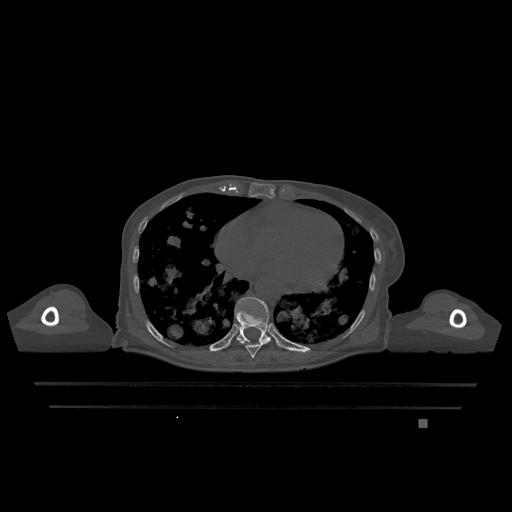
CT including the spine, one axial slice; slice 668 of 1317 in the series (ordered by position); bone window (W 1800 / L 400 HU); 0.5 mm slice thickness; 512 × 512 image matrix, field of view 500 × 500 mm. Patient: female, 74 years. Case-level facts recorded for this patient, not image findings: primary cancer: lung; vertebrae with lytic lesions (as recorded): T1, T4, T5, T6, L4, L5.
Annotated regions visible in this slice (semi-automatic segmentation, software-assisted and operator-edited):
- T10 vertebra: bounding box <235,297,271,342> (left, top, right, bottom; pixels)
- T9 vertebra: <236,338,271,358>